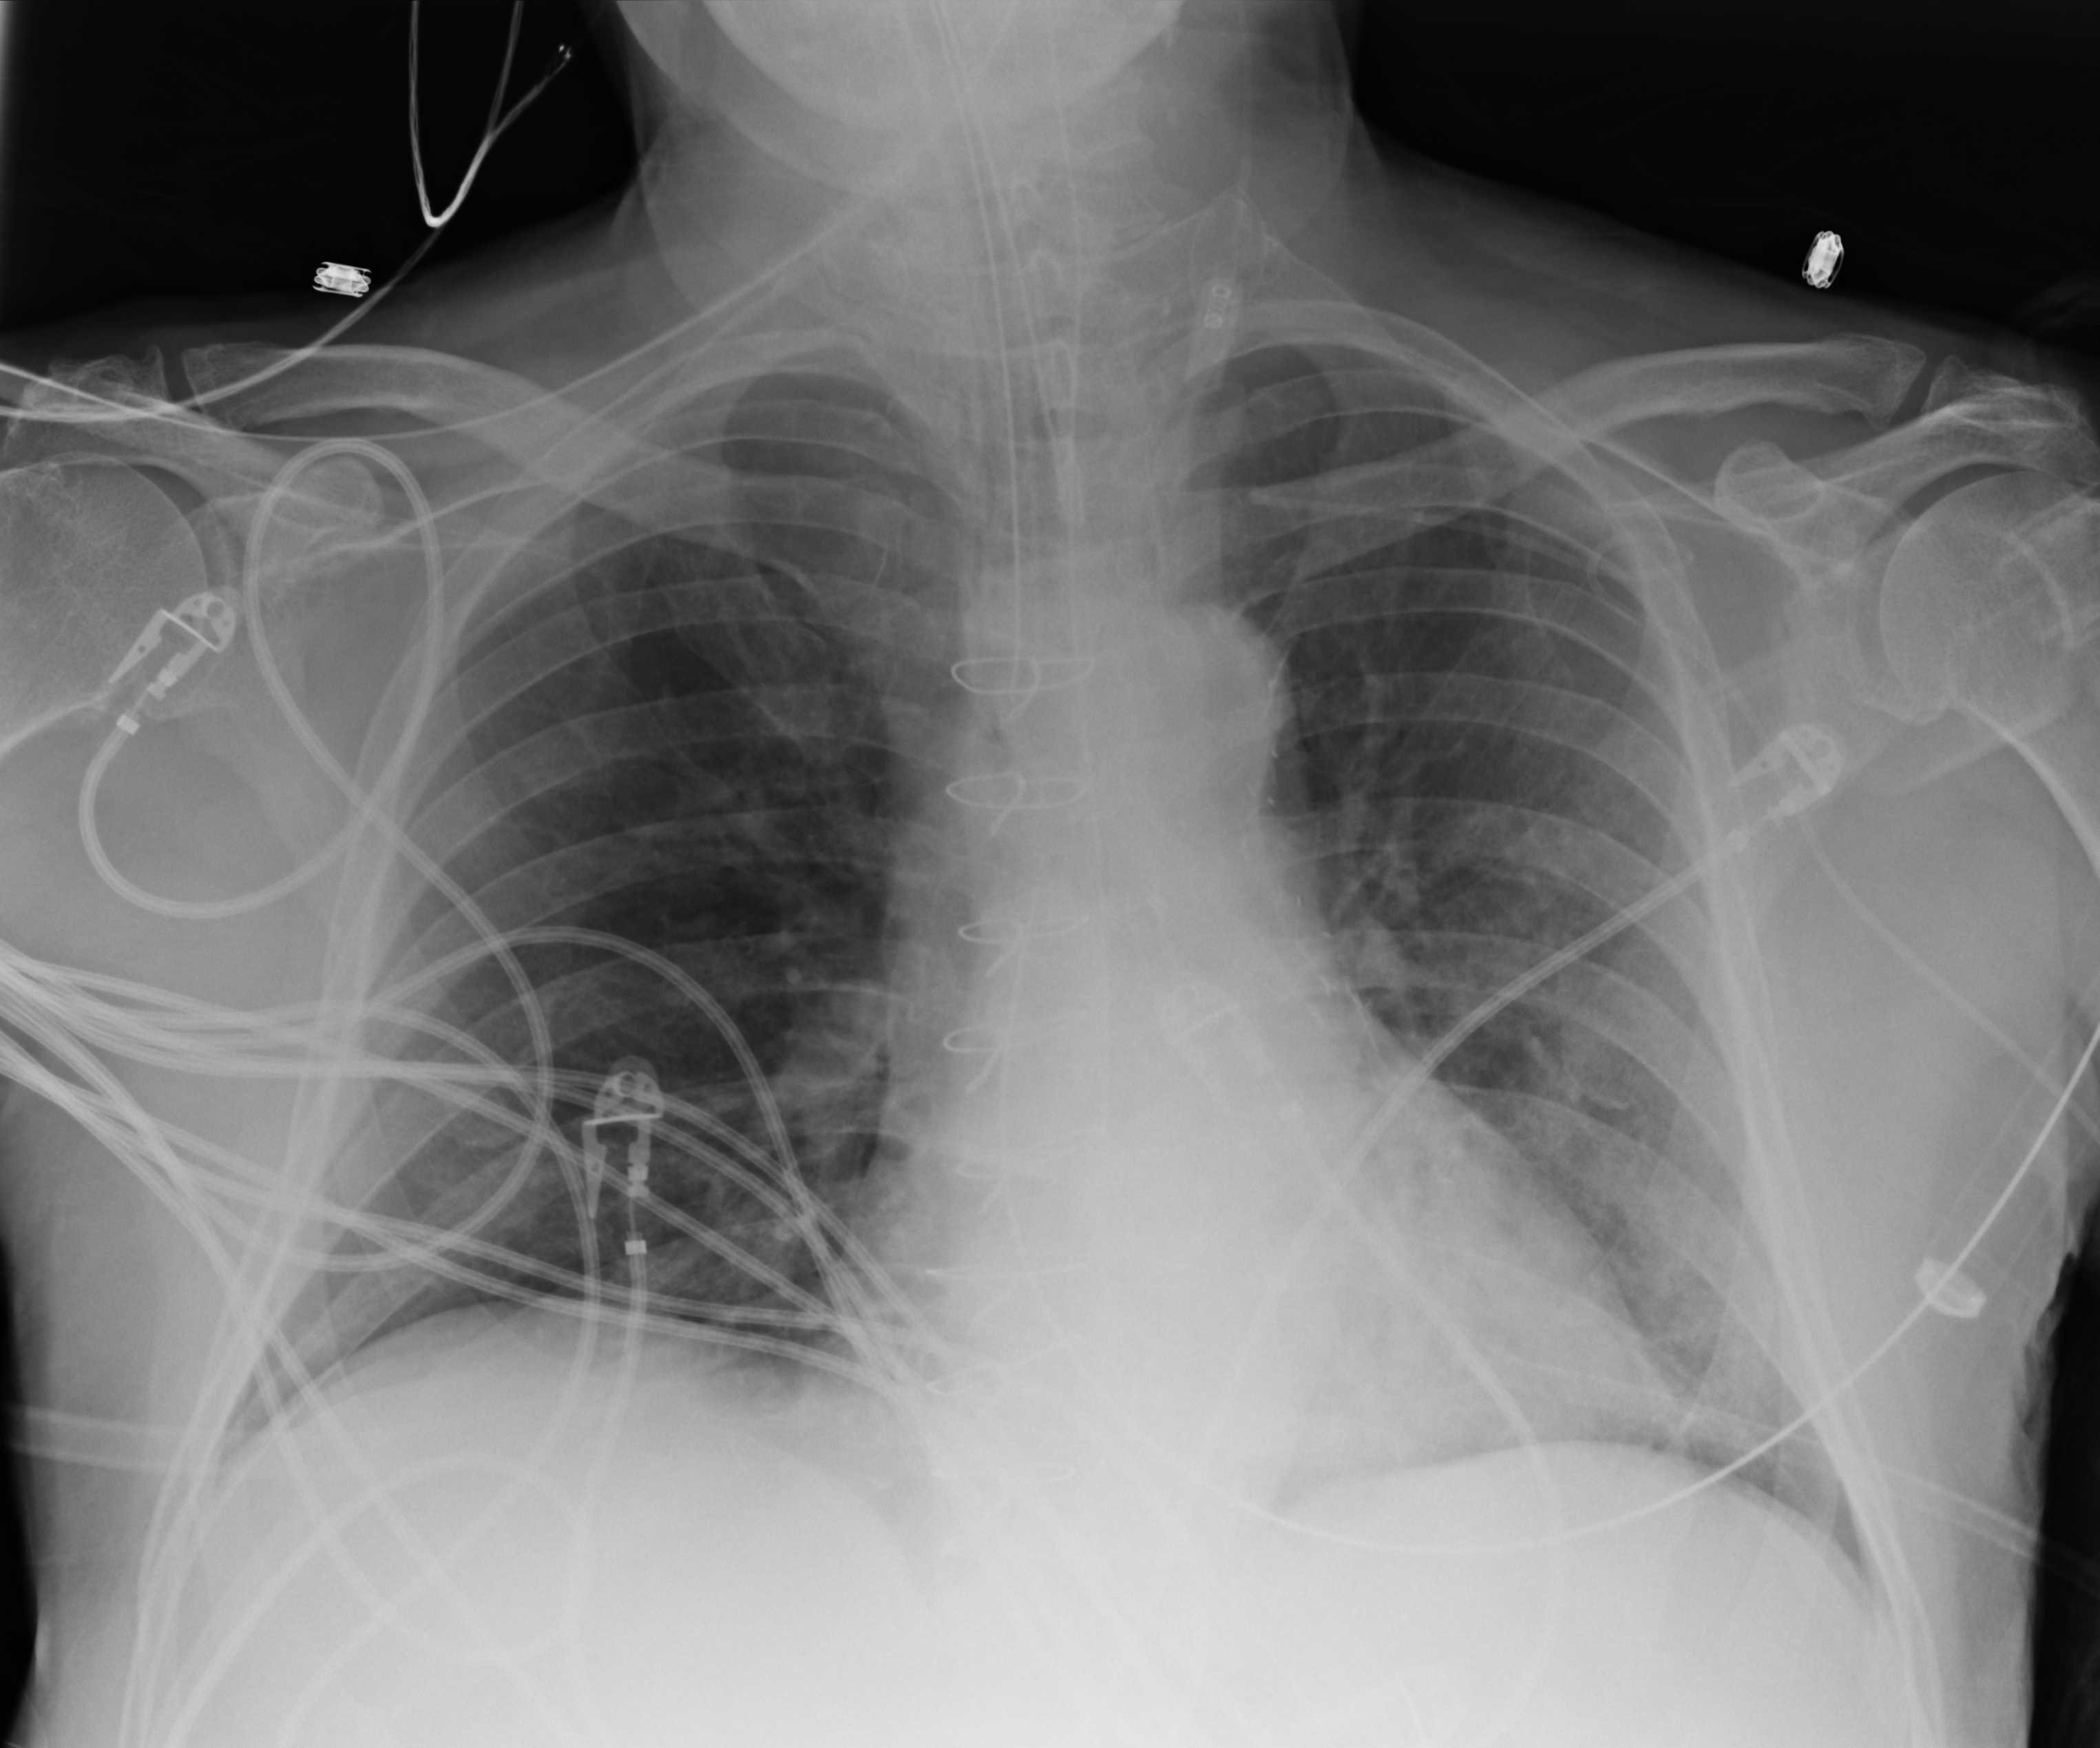
Portable chest radiograph, anteroposterior (AP) projection. Male patient hospitalised with COVID-19, age 60–74 years.
Hospital-stay facts (about this admission, not read from this image; timing relative to this image not recorded): smoking status (admission record): never; chronic kidney disease (admission record): no; COPD (admission record): no.